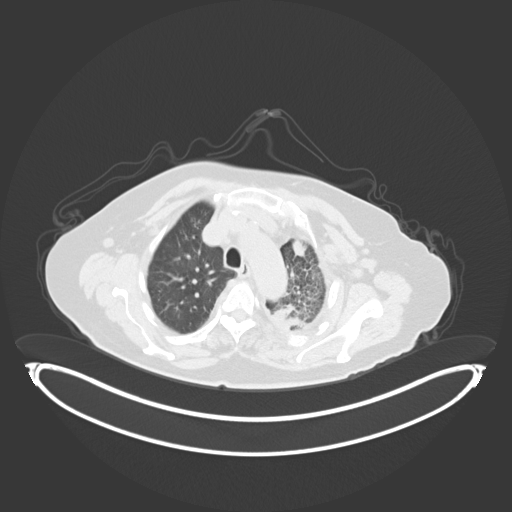
Chest CT, one axial slice. Position 222 of 284 along the scan axis. Reconstruction kernel B30f. Lung window (W 1500 / L -600 HU). 3 mm slice thickness. 512 × 512 image matrix, field of view 500 × 500 mm. Patient: female, 75 years. From the clinical record (not read from this slice): clinical TNM (as recorded): T3 N3 M1.
Structures marked on this image (rectangle marked by the reading radiologist):
- lung tumour (recorded histology: adenocarcinoma): bounding box [x1, y1, x2, y2] px = [268, 295, 309, 333]